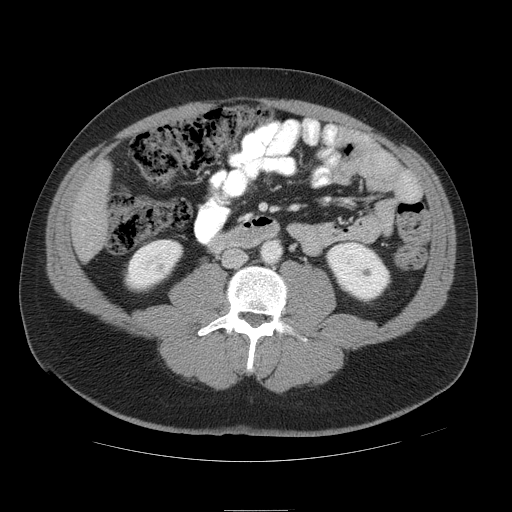
Contrast-enhanced abdominal CT, one axial slice. Position 12 of 49 along the scan axis. Reconstruction kernel STANDARD. 120 kVp. Intravenous contrast given. Soft-tissue window (W 400 / L 40 HU). 5 mm slice thickness. 512 × 512 image matrix, field of view 425 × 425 mm. Male patient, age 52 years. From the clinical record (not read from this slice): diagnosis: colorectal cancer liver metastases, imaged before liver resection; multiple liver metastases: yes; largest metastasis: 5.1 cm.
Structures marked on this image (expert manual segmentation):
- liver: box from (x=72, y=164) to (x=111, y=260) px